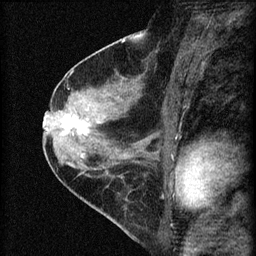
Breast MRI (dynamic contrast-enhanced), one sagittal slice; slice 33 of 60 in the series (ordered by position); dynamic contrast-enhanced series, image 2 of 4 at this slice position (ordered by acquisition); 1.5 T; TE 4.2 ms, TR 8.2 ms; 2 mm slice thickness; 256 × 256 image matrix, field of view 180 × 180 mm. Patient: female, 45 years.
Annotated regions visible in this slice (semi-automatic segmentation, software-assisted and operator-edited):
- analysis volume of interest (the breast-tissue region the enhancement analysis was run in; not a lesion): bounding box [x1, y1, x2, y2] px = [58, 107, 98, 147]
- tumour enhancement mask (voxels above the 70 % enhancement threshold inside the analysis volume of interest): [62, 114, 89, 136]